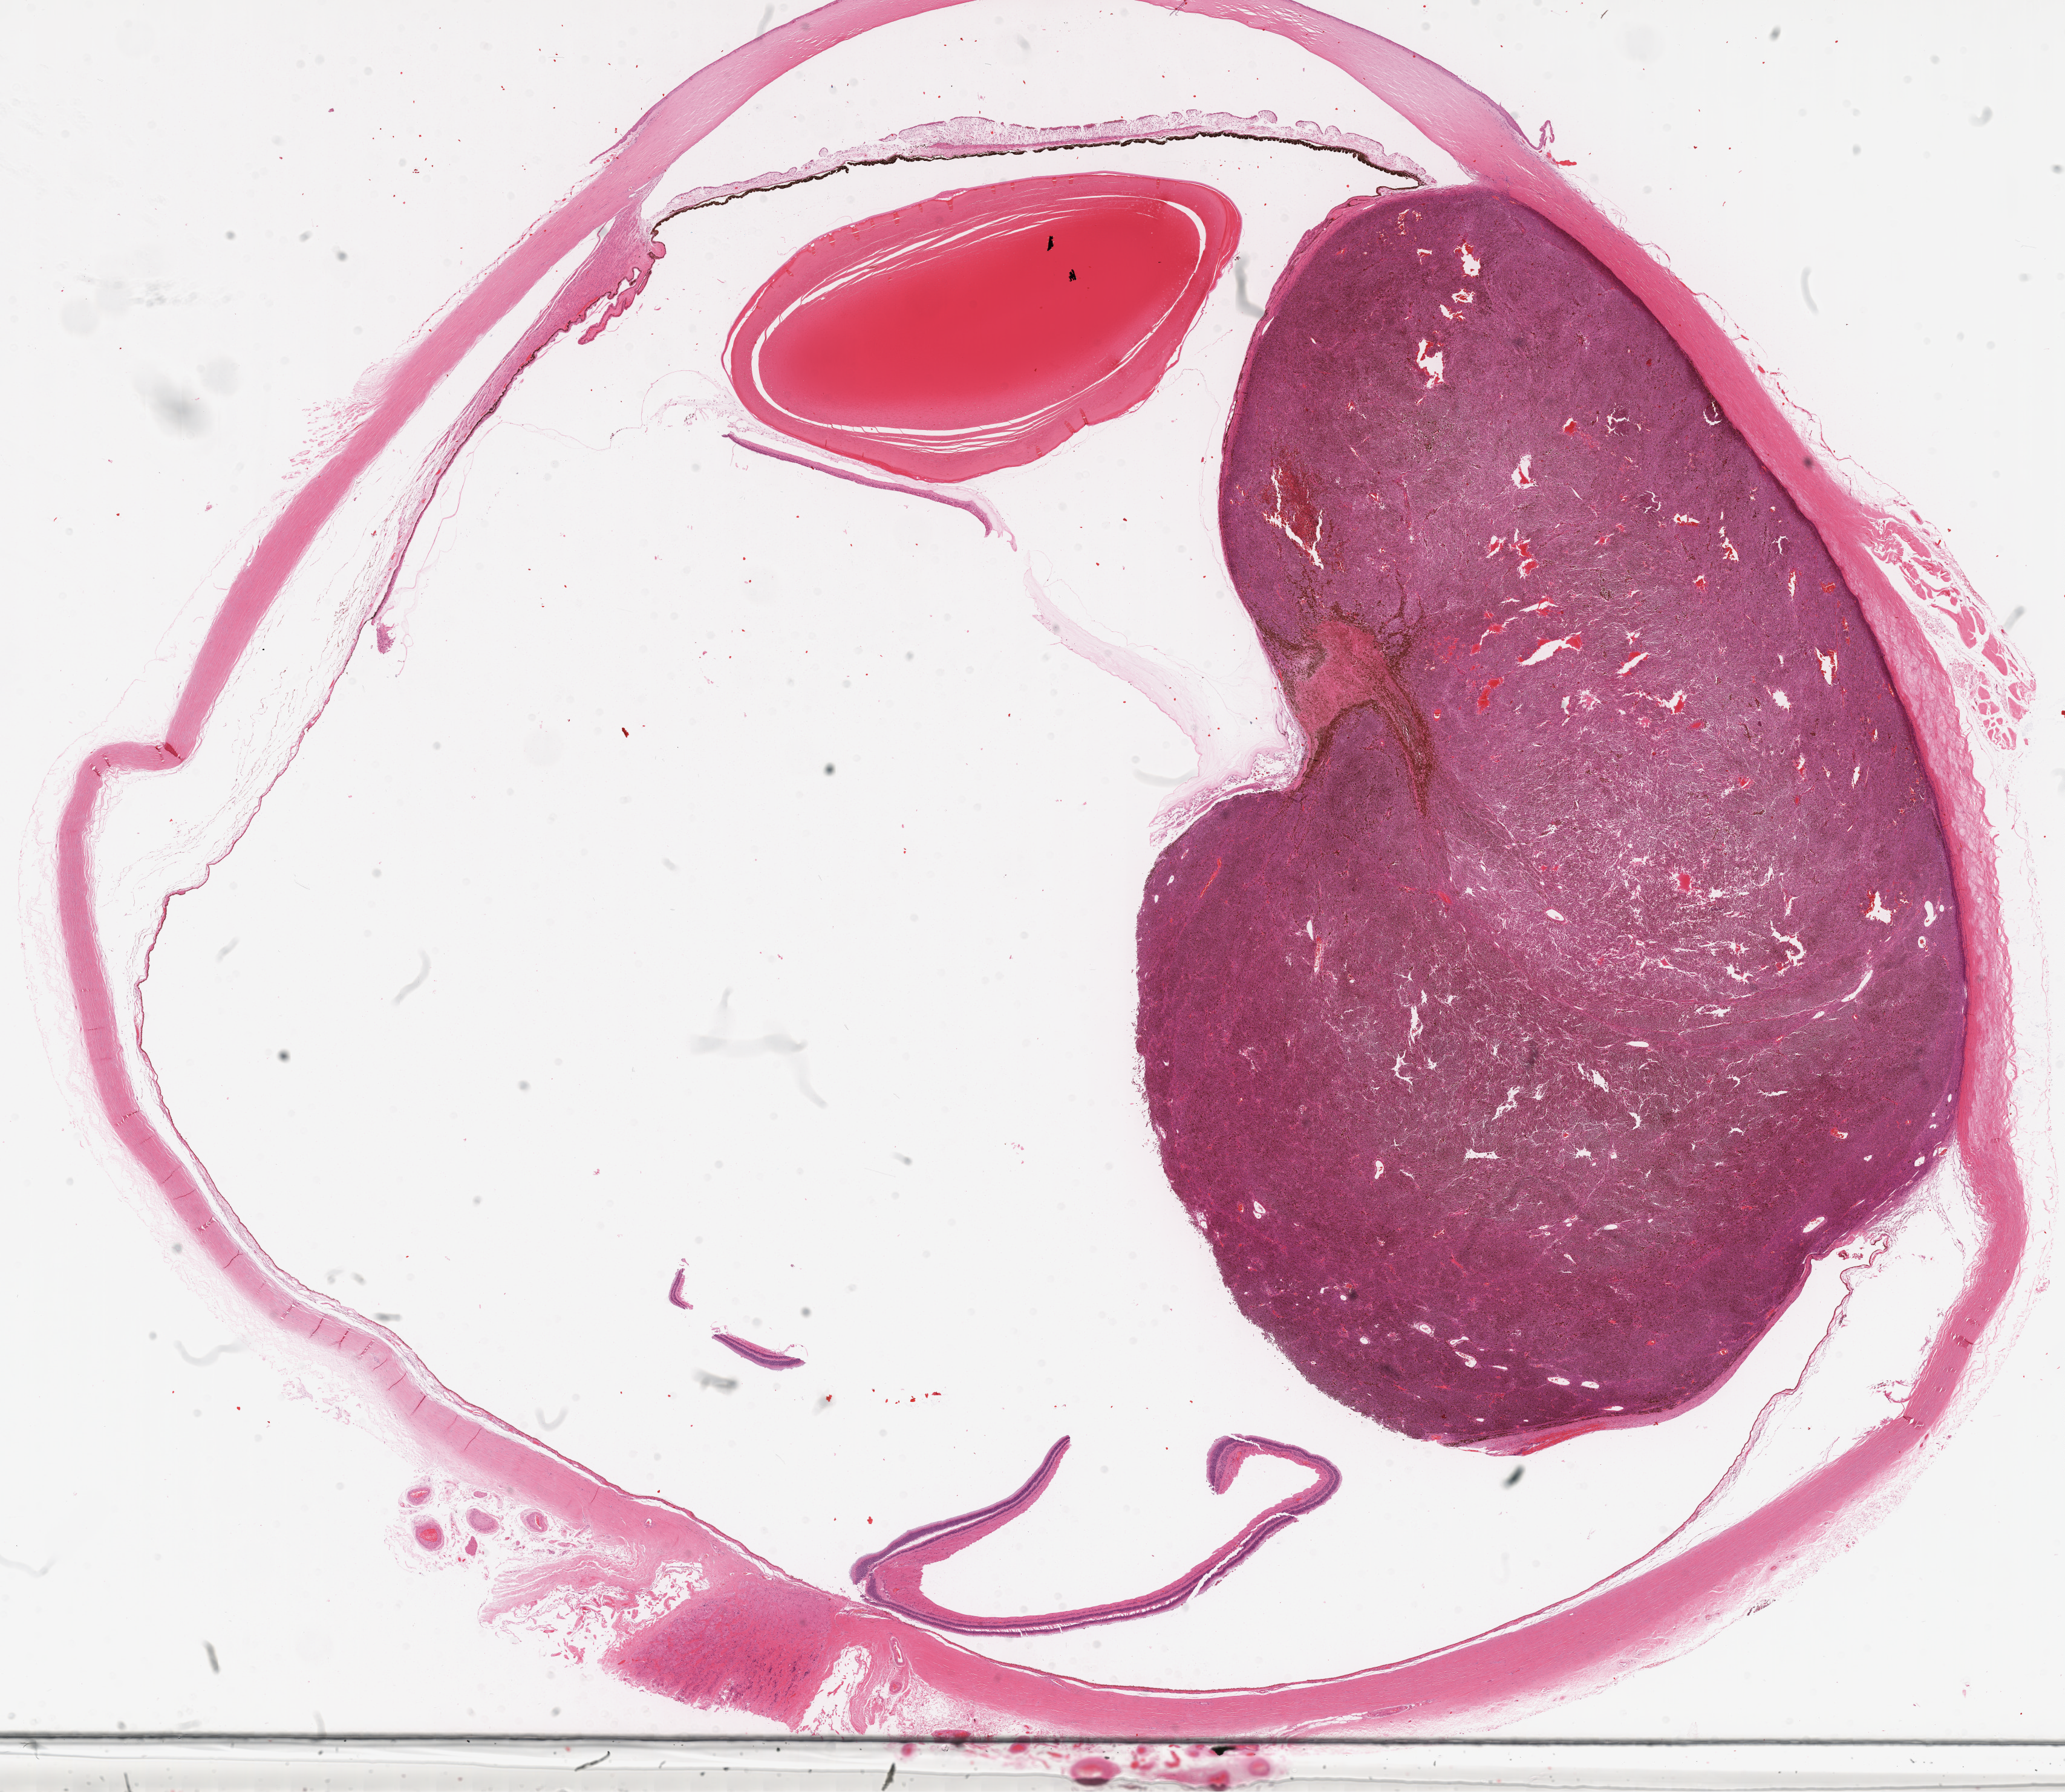
Whole-slide histology image, Hematoxylin and eosin (H&E) stained — shown as a low-resolution overview of the whole scanned area (about 27.5 x 23.9 mm); formalin-fixed paraffin-embedded (FFPE) diagnostic section; primary tumour sample from the uvea. Male patient; age at initial diagnosis 86 years.
Histologic diagnosis: Mixed epithelioid and spindle cell melanoma (choroid).